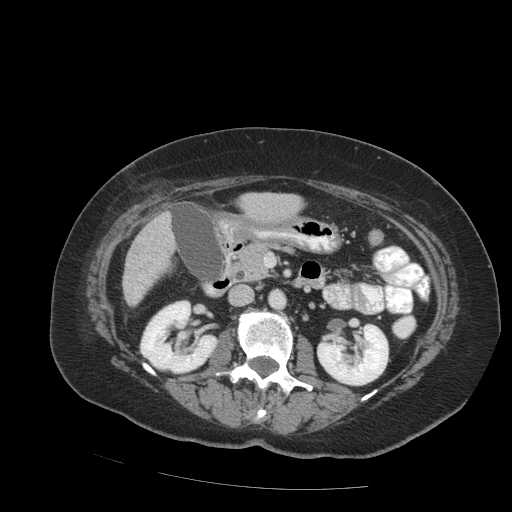
Contrast-enhanced abdominal CT (liver protocol), one axial slice; position 31 of 99 along the scan axis; 140 kVp; soft-tissue window (W 400 / L 40 HU); 512 × 512 image matrix, field of view 400 × 400 mm. Case-level facts recorded for this patient, not image findings: diagnosis: hepatocellular carcinoma (patient treated with transarterial chemoembolisation; whether this scan precedes or follows treatment is not stated here); TNM stage (as recorded): Stage-IVB; Child-Pugh class: A; tumour nodularity: uninodular.
Structures marked on this image (semi-automatically segmented with operator editing):
- liver parenchyma outside the tumour (the mass and vessels are separate outlines, so this box may not span the whole liver): bounding box <122,212,174,306> (left, top, right, bottom; pixels)